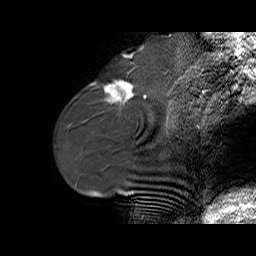
Breast MRI (dynamic contrast-enhanced), one sagittal slice. Dynamic contrast-enhanced series, time point 2 of 6 at this slice position (early post-contrast). 1.5 T. TE 5.5 ms, TR 32.9 ms. 256 × 256 image matrix, field of view 240 × 240 mm. Female patient. From the clinical record (not read from this slice): setting: breast cancer imaged before/during neoadjuvant chemotherapy; receptor status: HER2-positive.
Annotated regions visible in this slice (semi-automatic segmentation, software-assisted and operator-edited):
- analysis volume of interest (the breast-tissue region the enhancement analysis was run in; not a lesion): box from (x=96, y=74) to (x=141, y=114) px
- tumour enhancement mask (voxels above the 100 % enhancement threshold inside the analysis volume of interest): (x=104, y=81)–(x=134, y=102)